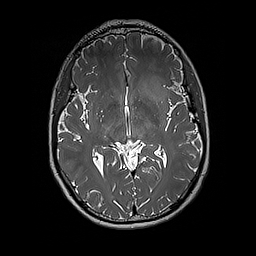
Brain MRI from a brain-tumour surgery series, one axial slice; position 103 of 192 along the scan axis; 256 × 256 image matrix, field of view 250 × 250 mm. Case-level facts recorded for this patient, not image findings: histopathology: Glioblastoma; WHO grade: 4; IDH mutation: no; tumour location: Left Insular.
Outlined on this slice (expert manual segmentation):
- tumour: bounding box (x1, y1, x2, y2) in pixels: (140, 76, 171, 113)